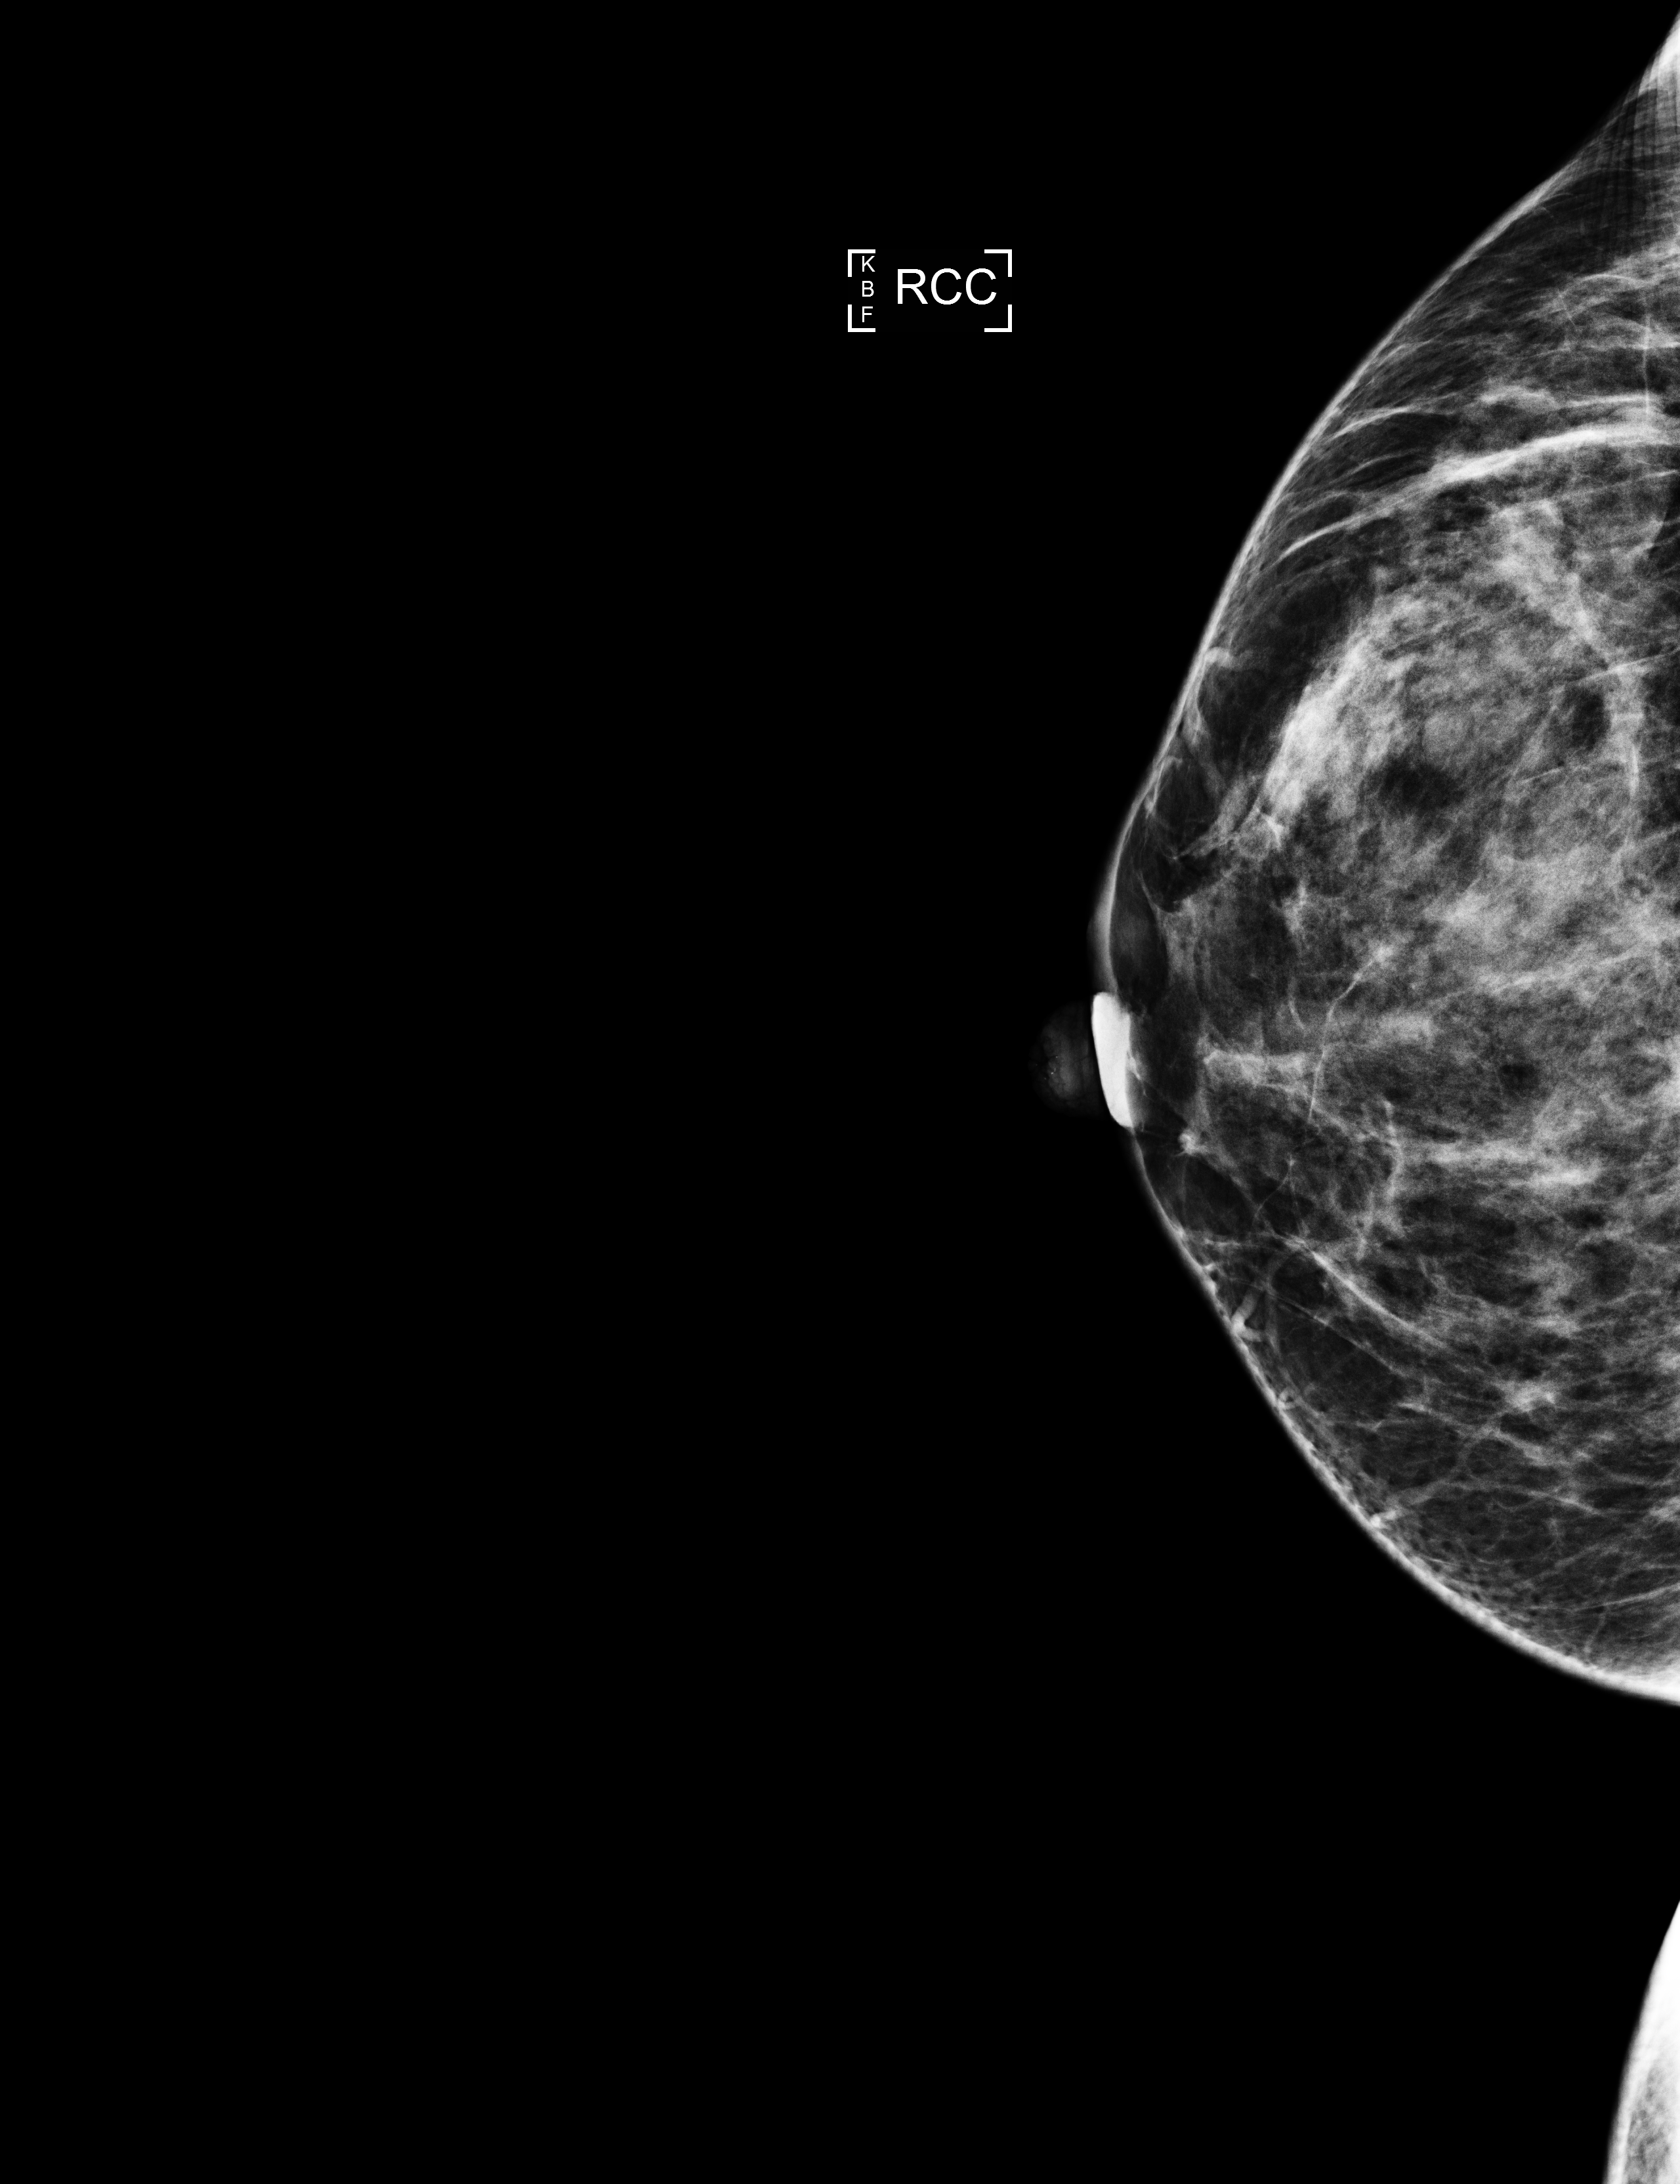
Full-field digital mammogram (FFDM), right breast, craniocaudal (CC) view, annual screening mammography examination, compressed breast thickness 47 mm. Patient: female, 49 years.
- BI-RADS breast density category at the screening exam (both breasts, scale 1–4): 4
- final BI-RADS assessment for this screening round (tomosynthesis exam, both breasts): category 1
- recall: no recall after this screen